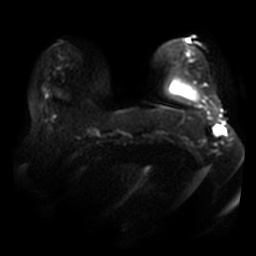
Breast MRI, one axial slice; slice 8 of 40 in the series (ordered by position); diffusion-weighted series; image 2 of 4 stored at this slice position (different b-values; order by instance number); 3 T; 5 mm slice thickness; 256 × 256 image matrix, field of view 400 × 400 mm. Female patient.
Outlined on this slice (expert manual segmentation):
- tumour on diffusion-weighted imaging: bounding box [x1, y1, x2, y2] px = [223, 127, 226, 134]